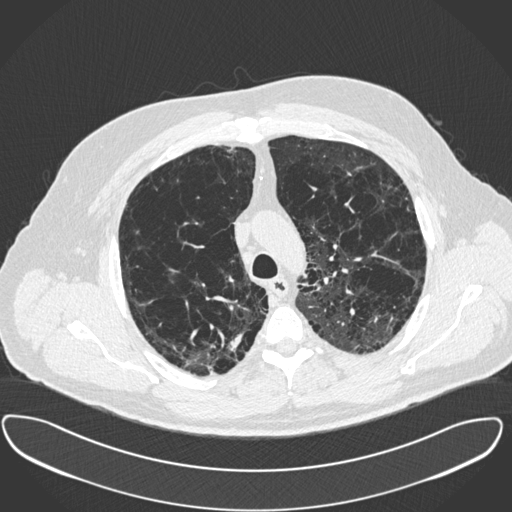
Low-dose screening chest CT, one axial slice. Reconstruction kernel B30f. Lung window (W 1500 / L -600 HU). 1 mm slice thickness. 512 × 512 image matrix, field of view 408 × 408 mm.
Annotated regions visible in this slice (manually delineated by an expert):
- lesion 1 (tumor, upper lobe of right lung): bounding box (x1, y1, x2, y2) in pixels: (228, 334, 243, 352)